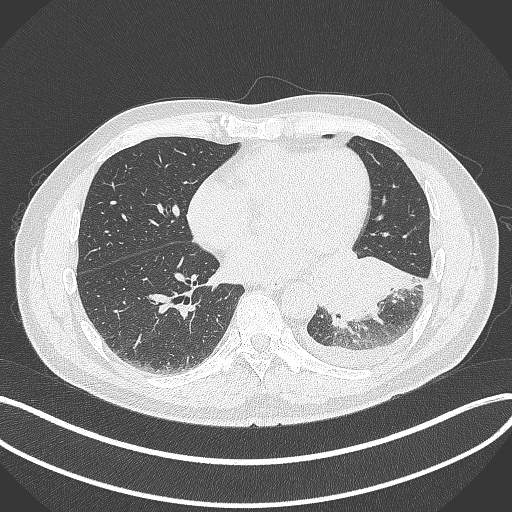
Chest CT, one axial slice; slice 142 of 342 in the series (ordered by position); reconstruction kernel B70f; lung window (W 1500 / L -600 HU); 1 mm slice thickness; 512 × 512 image matrix, field of view 400 × 400 mm. Male patient, age 58 years. Case-level facts recorded for this patient, not image findings: clinical TNM (as recorded): T3 N1 M1b; histopathological grade: G3.
Outlined on this slice (rectangle marked by the reading radiologist):
- lung tumour (recorded histology: small cell carcinoma): box from (x=305, y=246) to (x=419, y=330) px